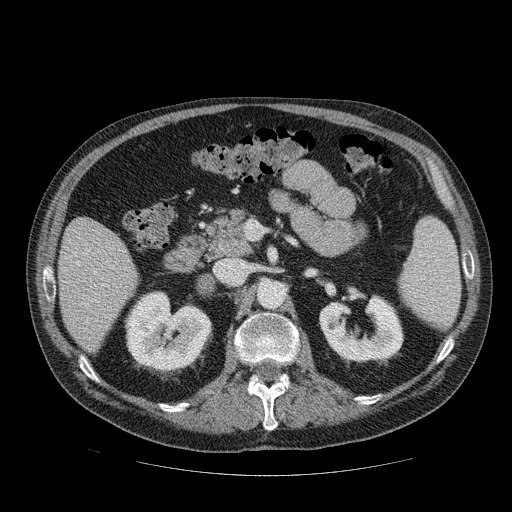
Contrast-enhanced abdominal CT, one axial slice; position 44 of 111 along the scan axis; reconstruction kernel STANDARD; intravenous contrast given; soft-tissue window (W 400 / L 40 HU); 2.5 mm slice thickness; 512 × 512 image matrix. Patient: male, 56 years. Case-level facts recorded for this patient, not image findings: diagnosis: adrenocortical carcinoma; tumour side: right adrenal; tumour size at pathology: 9 cm; Ki-67 index: 48 %; stage (as recorded): 4.
Outlined on this slice (semi-automatically segmented with operator editing):
- mass: bounding box (x1, y1, x2, y2) in pixels: (197, 276, 213, 293)